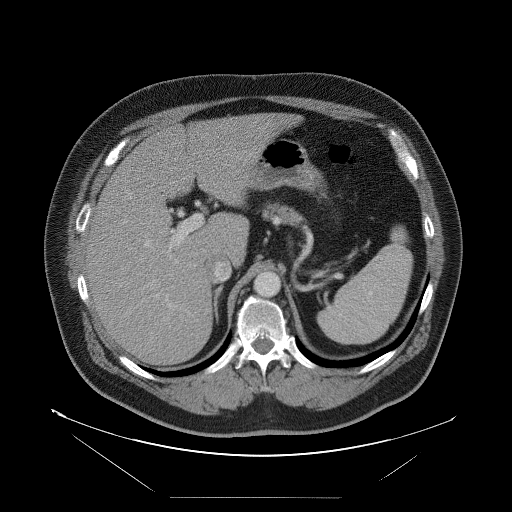
Contrast-enhanced abdominal CT, one axial slice. Slice 63 of 114 in the series (ordered by position). 120 kVp. Intravenous contrast given. Soft-tissue window (W 400 / L 40 HU). 5 mm slice thickness. 512 × 512 image matrix, field of view 500 × 500 mm. Male patient, age 61 years. Case-level facts recorded for this patient, not image findings: diagnosis: colorectal cancer liver metastases, imaged before liver resection; multiple liver metastases: no; largest metastasis: 6.5 cm; disease in both lobes: yes.
Structures marked on this image (expert manual segmentation):
- hepatic veins: bounding box [x1, y1, x2, y2] px = [144, 240, 150, 247]
- liver: [87, 114, 289, 366]
- planned liver remnant (the part of the liver to remain after resection): [145, 114, 289, 257]
- portal vein (with intrahepatic branches): [154, 214, 203, 302]